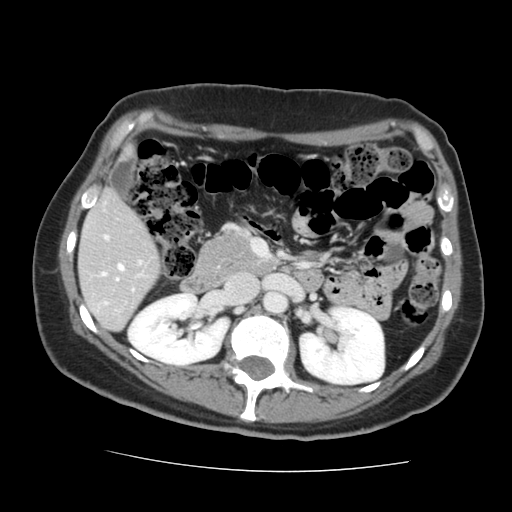
Contrast-enhanced abdominal CT, one axial slice; slice 70 of 144 in the series (ordered by position); 120 kVp; intravenous contrast given; soft-tissue window (W 400 / L 40 HU); 2.5 mm slice thickness; 512 × 512 image matrix, field of view 333 × 333 mm. Female patient, age 46 years. Case-level facts recorded for this patient, not image findings: diagnosis: colorectal cancer liver metastases, imaged before liver resection; multiple liver metastases: no; largest metastasis: 2.8 cm.
Structures marked on this image (outlined manually by an expert reader):
- liver: box from (x=79, y=193) to (x=160, y=330) px
- planned liver remnant (the part of the liver to remain after resection): (x=79, y=193)–(x=160, y=323)
- portal vein (with intrahepatic branches): (x=101, y=236)–(x=141, y=281)